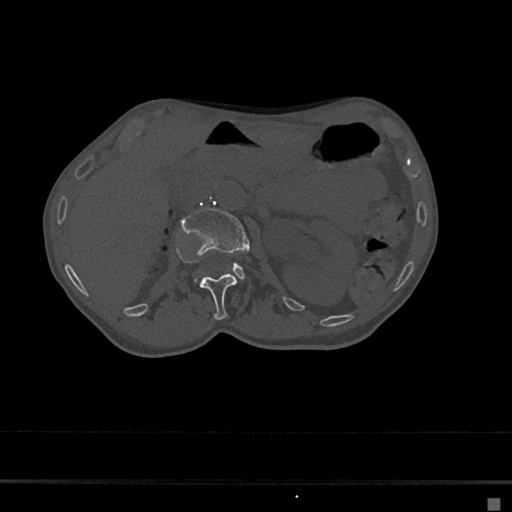
CT including the spine, one axial slice; slice 51 of 797 in the series (ordered by position); reconstruction kernel Br40s/3; bone window (W 1800 / L 400 HU); 0.5 mm slice thickness; 512 × 512 image matrix, field of view 360 × 360 mm. Patient: female, 68 years. From the clinical record (not read from this slice): primary cancer: renal.
Structures marked on this image (semi-automatic segmentation, software-assisted and operator-edited):
- L1 vertebra: bounding box [x1, y1, x2, y2] px = [199, 273, 236, 321]
- L2 vertebra: [181, 207, 250, 278]